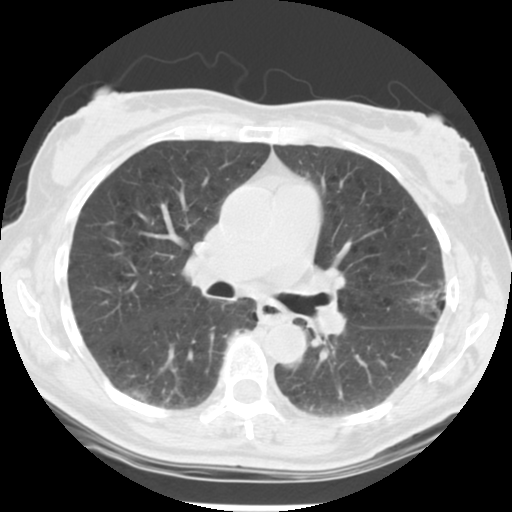
Low-dose screening chest CT, axial slice. Second annual screen. Lung window (W 1500 / L -600 HU). 120 kVp. 512 × 512 image matrix. Female participant, aged 61 years at enrolment. Current smoker at enrolment.
Expert reader's lesion annotation, bounding box (x1, y1, x2, y2) in pixels: (402, 272, 464, 332). Reader record for this screening exam (exam-level; its link to the box is not recorded): non-calcified nodule or mass ≥4 mm, left upper lobe, 15 × 15 mm, poorly defined margins, mixed attenuation, pre-existing on the prior screen: no. Official screen result: positive, other. Later outcome: lung cancer diagnosed 152 days after this screen — bronchiolo-alveolar adenocarcinoma, NOS, left upper lobe, well differentiated (G1), stage IA (AJCC 6th edition), 11 mm at pathology.